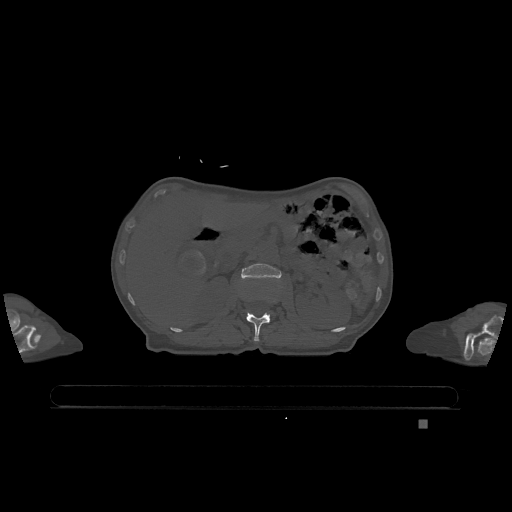
CT including the spine, one axial slice. Slice 457 of 1317 in the series (ordered by position). Bone window (W 1800 / L 400 HU). 0.5 mm slice thickness. 512 × 512 image matrix, field of view 500 × 500 mm. Female patient, age 74 years. From the clinical record (not read from this slice): primary cancer: lung; vertebrae with lytic lesions (as recorded): T1, T4, T5, T6, L4, L5.
Annotated regions visible in this slice (semi-automatically segmented with operator editing):
- L1 vertebra: box from (x=246, y=312) to (x=270, y=341) px
- L2 vertebra: (x=241, y=264)–(x=281, y=279)